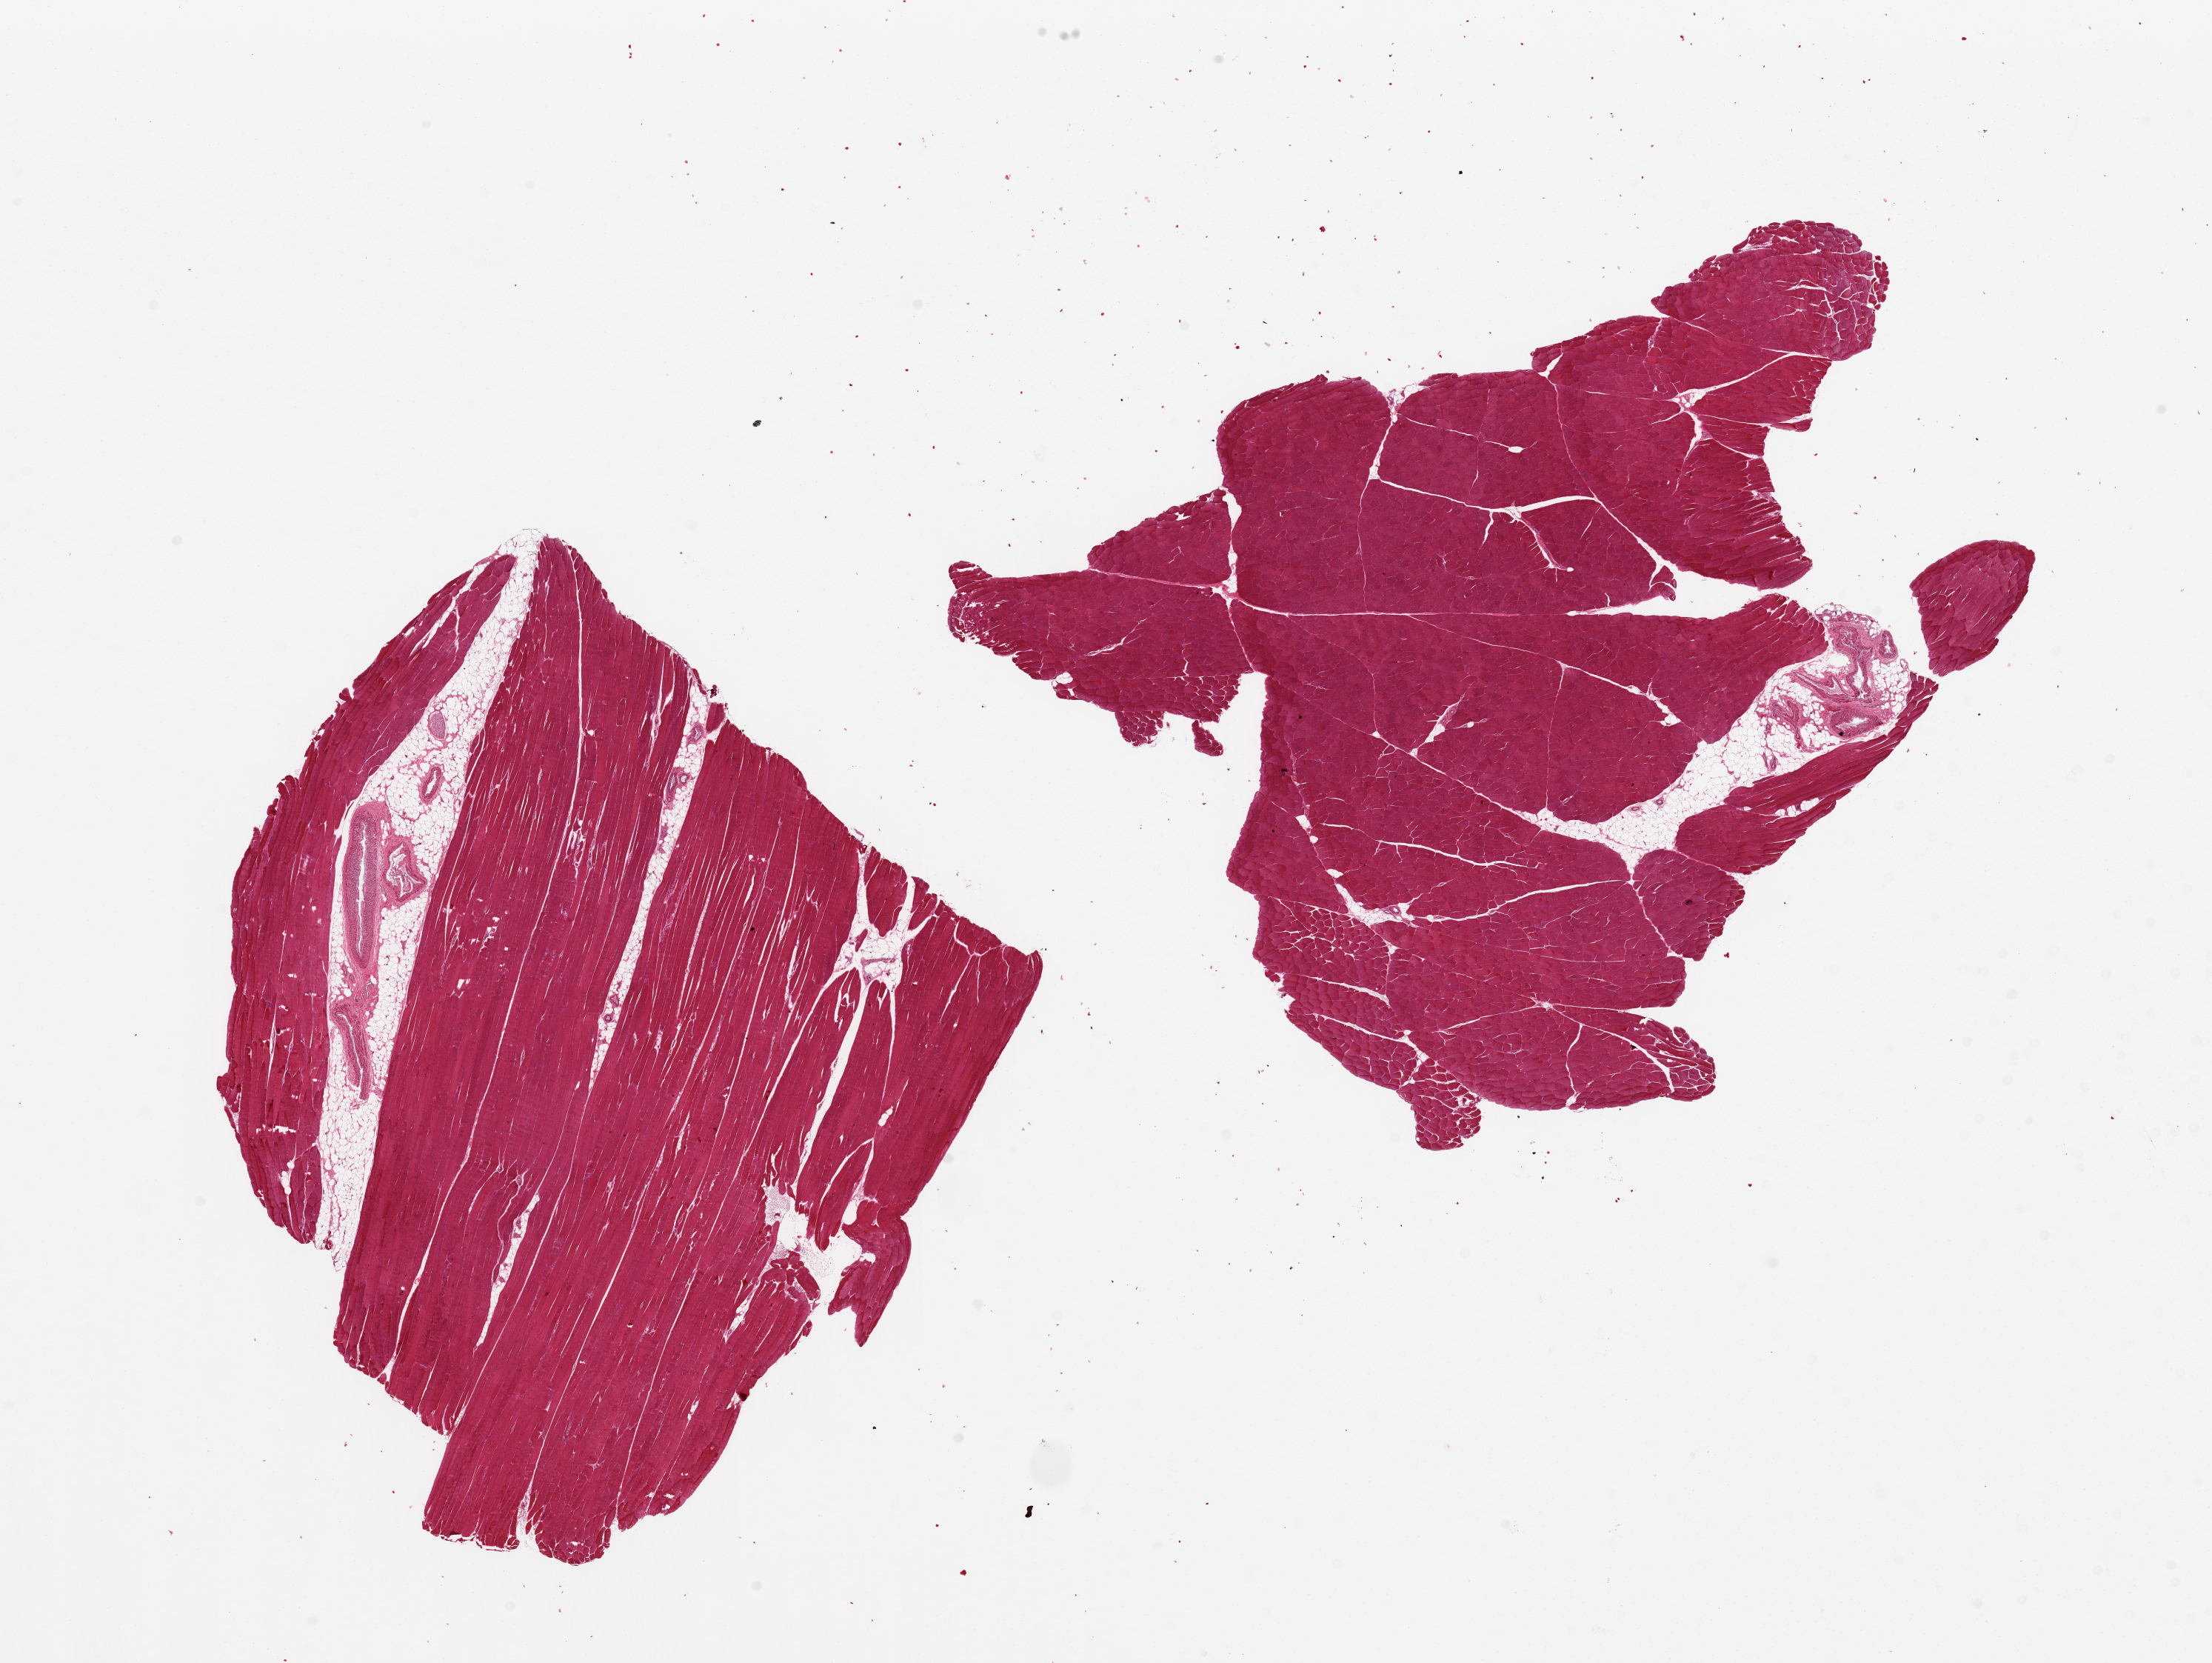
Whole-slide image, H&E stain, low-resolution overview of the scanned area, about 23.6 x 17.8 mm, PAXgene-fixed paraffin-embedded (PFPE) section, target tissue: skeletal muscle, tissue donor sample. Female donor.
Reviewer comment on this tissue sample: 2 pieces, ~5-10% interstitial foci of fat and vessels in each, but good specimens.